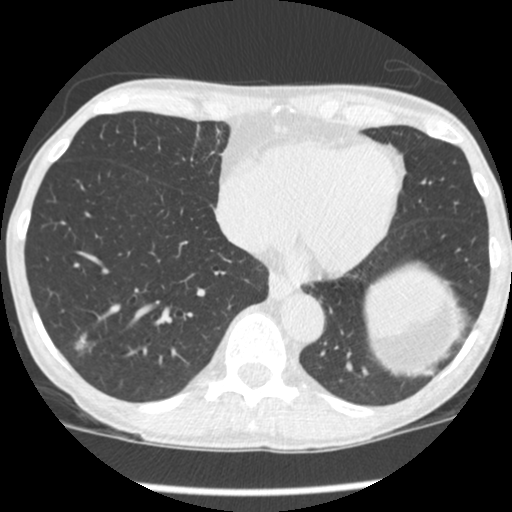
Low-dose screening chest CT, one axial slice; position 83 of 248 along the scan axis; reconstruction kernel STANDARD; 120 kVp; lung window (W 1500 / L -600 HU); 1.25 mm slice thickness; 512 × 512 image matrix, field of view 293 × 293 mm.
Annotated regions visible in this slice (outlined manually by an expert reader):
- lesion 1 (tumor, lower lobe of right lung): bounding box (x1, y1, x2, y2) in pixels: (75, 334, 87, 350)